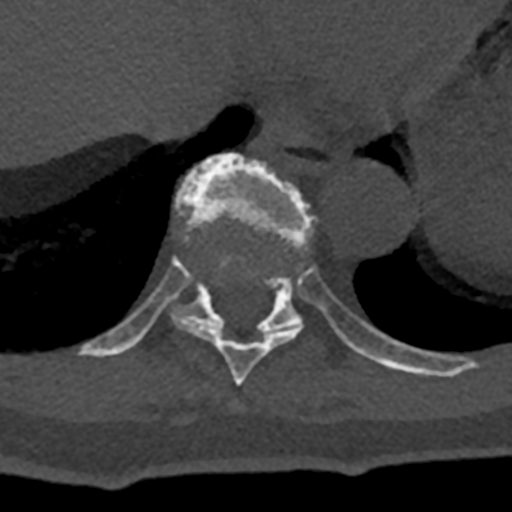
CT including the spine, one axial slice; slice 630 of 797 in the series (ordered by position); reconstruction kernel Br40s/3; bone window (W 1800 / L 400 HU); 0.5 mm slice thickness; 512 × 512 image matrix. Male patient, age 74 years. From the clinical record (not read from this slice): primary cancer: renal; vertebrae with lytic lesions (as recorded): T10, L1, L2, L3, L4, L5.
Annotated regions visible in this slice (semi-automatically segmented with operator editing):
- T10 vertebra: bounding box [x1, y1, x2, y2] px = [79, 152, 432, 375]
- T9 vertebra: [173, 256, 302, 385]